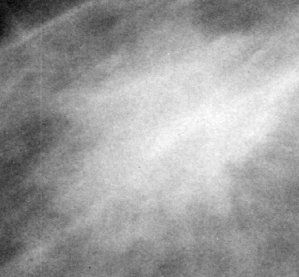
Crop from a digitized film mammogram around one marked abnormality; right breast; CC view; BI-RADS breast density category 2 (scale 1–4).
Finding: mass, shape irregular, margins ill defined / spiculated; BI-RADS assessment category 4; pathology (as recorded): malignant.